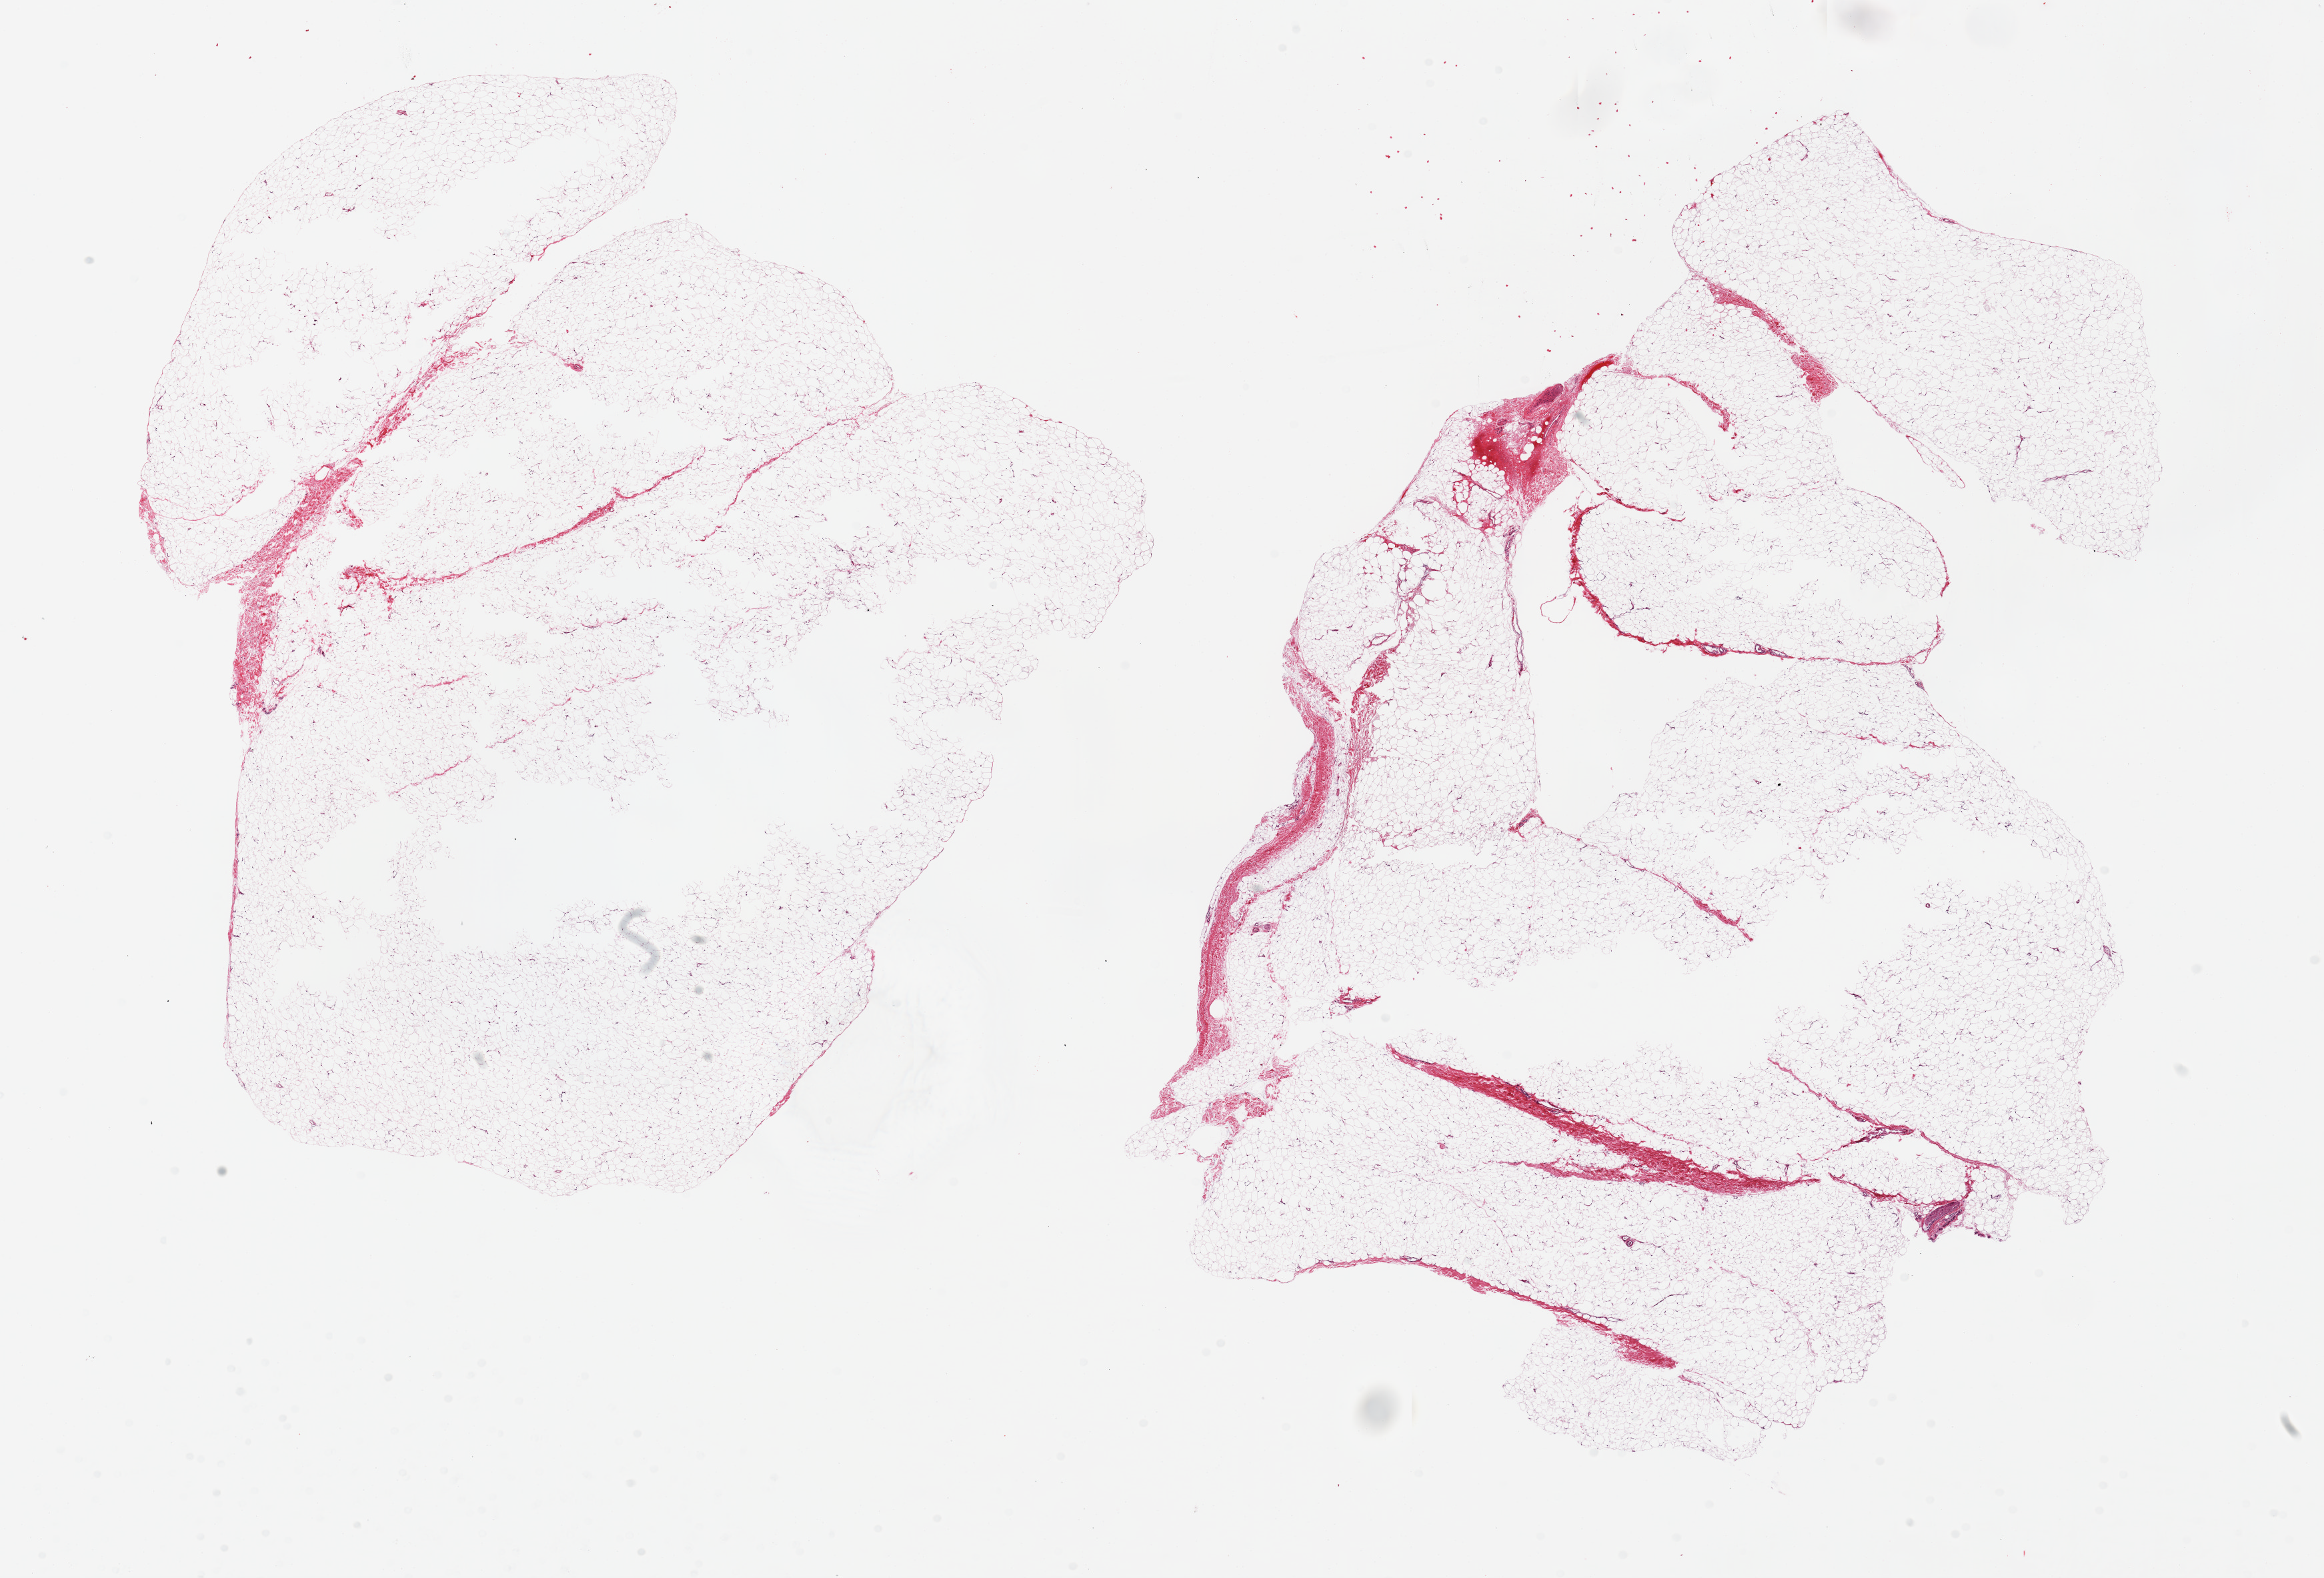
Digitized H&E-stained section, brightfield, whole scanned area (about 27.6 x 18.7 mm, slide scanned at 20x) shown as a low-resolution overview; PAXgene-fixed paraffin-embedded (PFPE) section; sampled site (target tissue): adipose tissue; tissue donor sample. Donor sex: male.
Pathologist's review note for this sample: 2 pieces ~13x11mm.